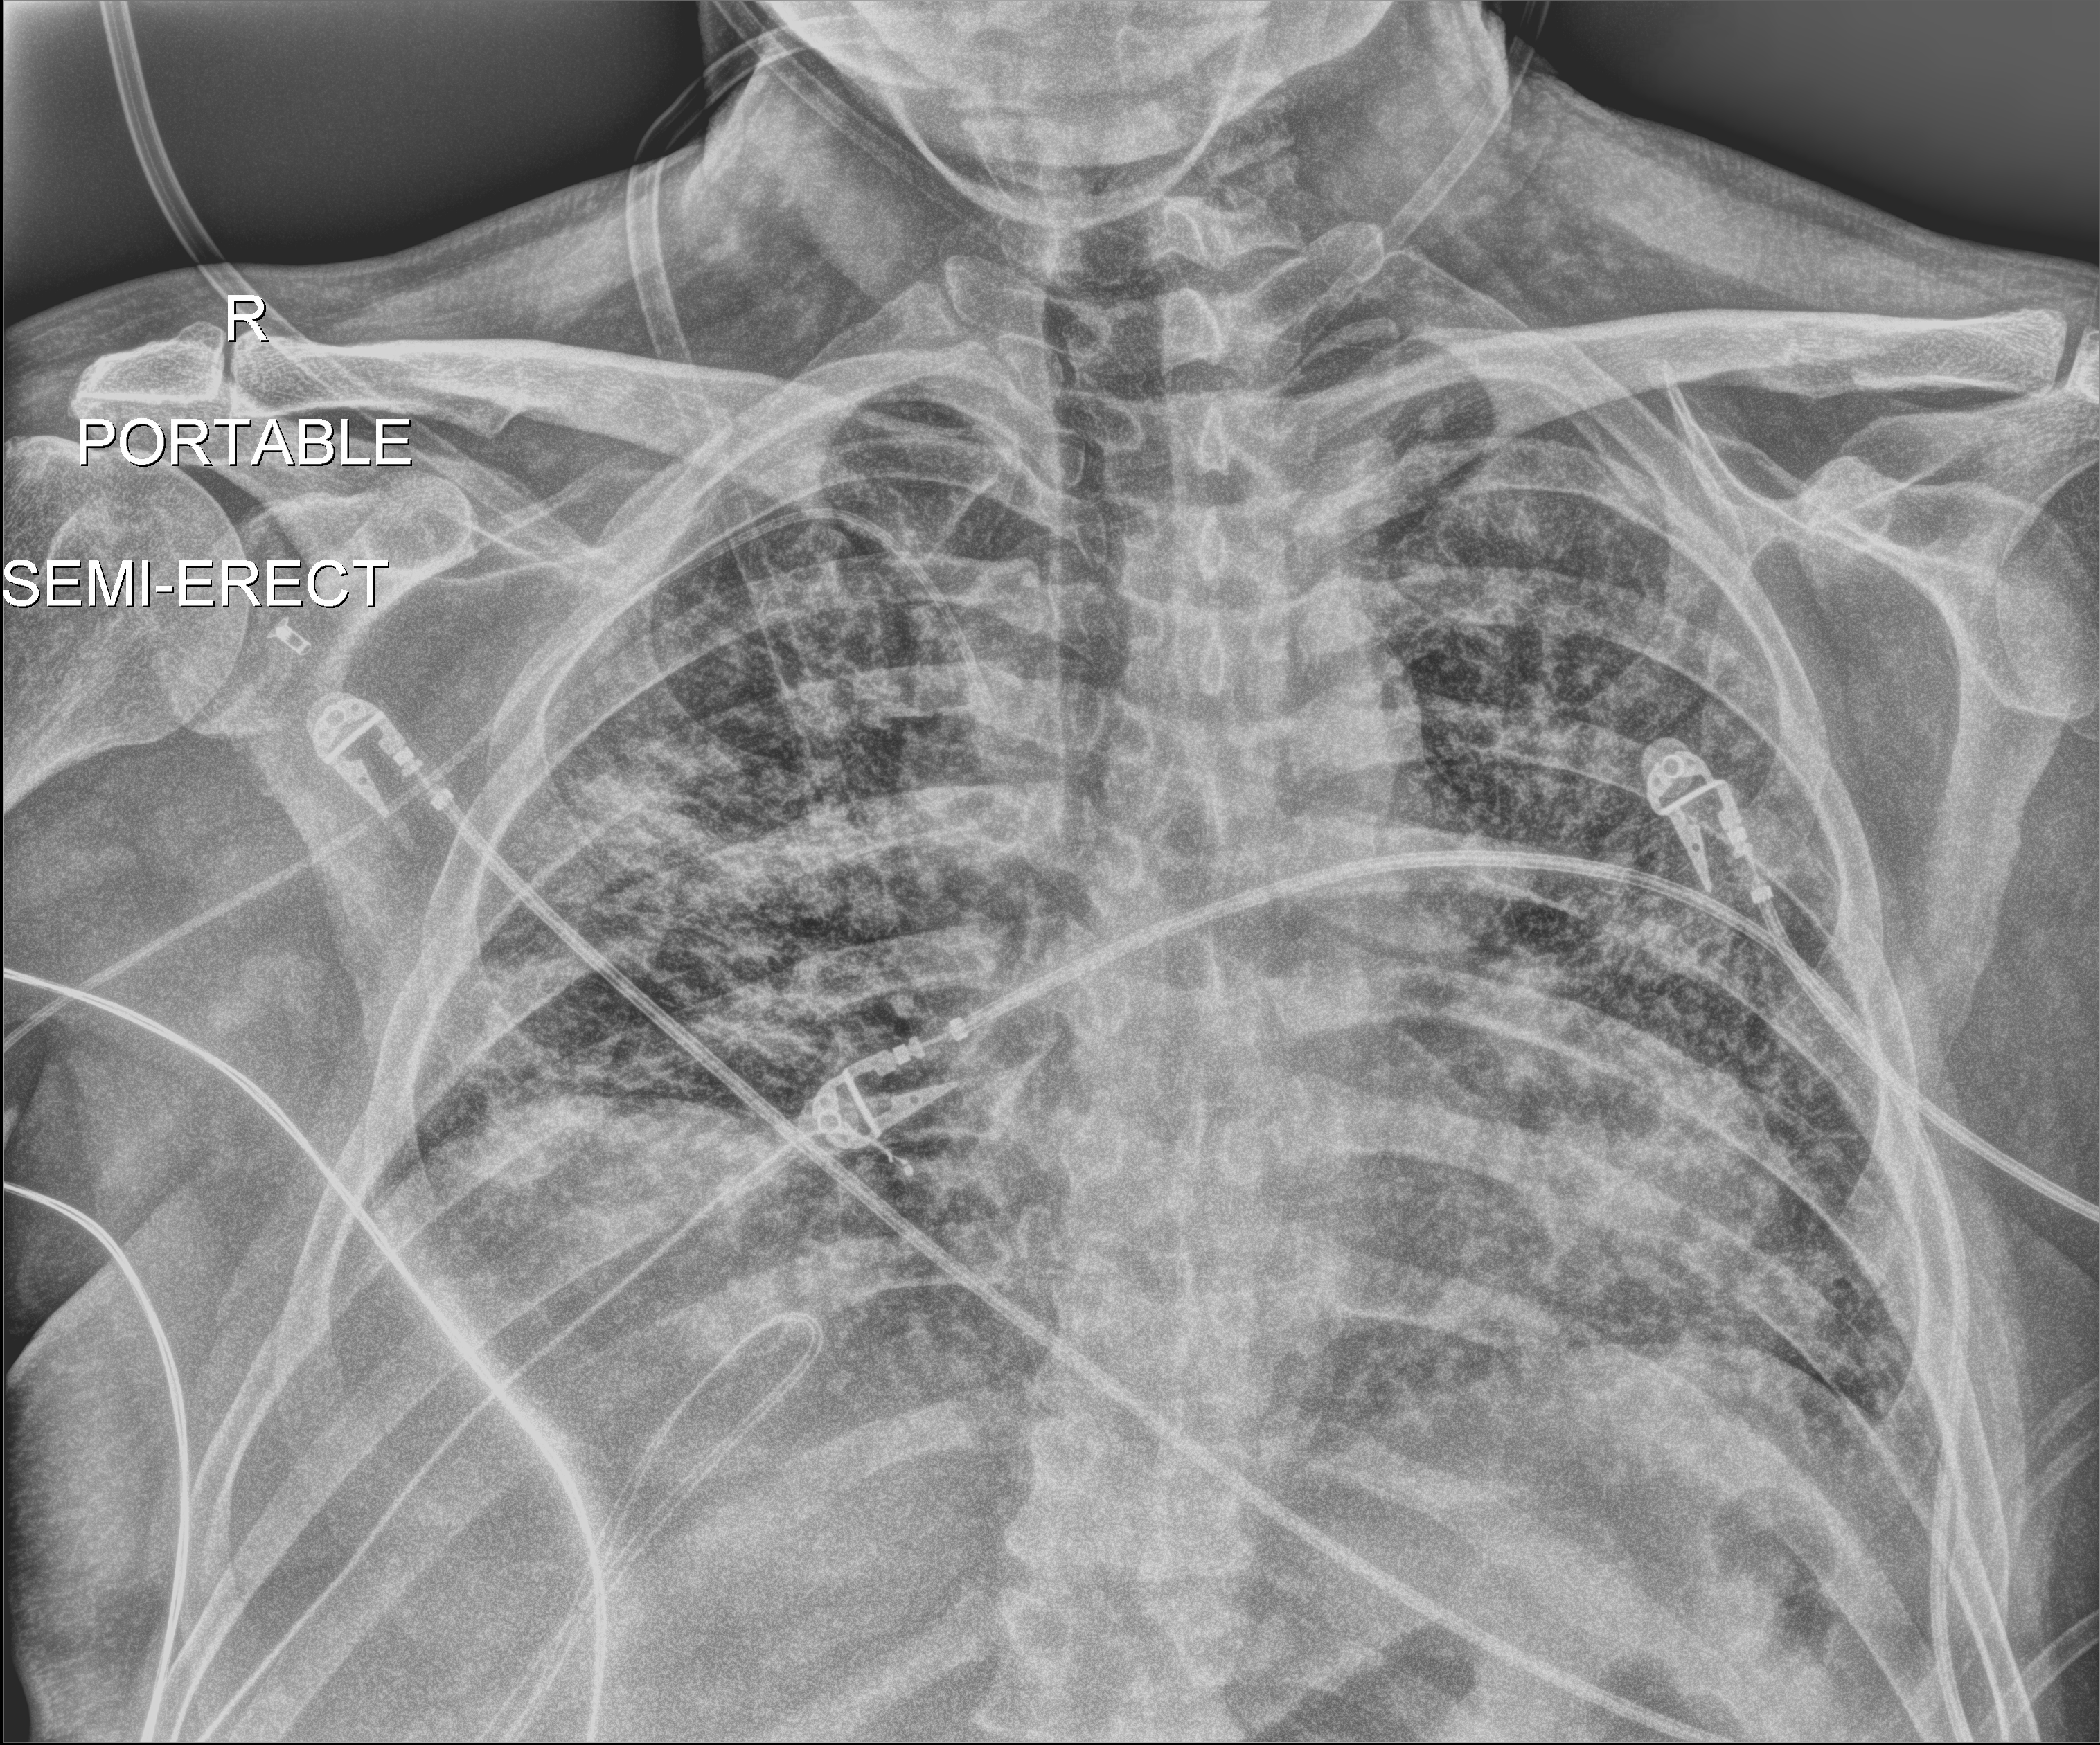
Chest radiograph; anteroposterior (AP) projection. Patient hospitalised with COVID-19; male, aged 18–59 years.
Admission-level facts for this patient (not findings on this image; timing relative to this image not recorded):
- mechanically ventilated during this hospital stay: yes